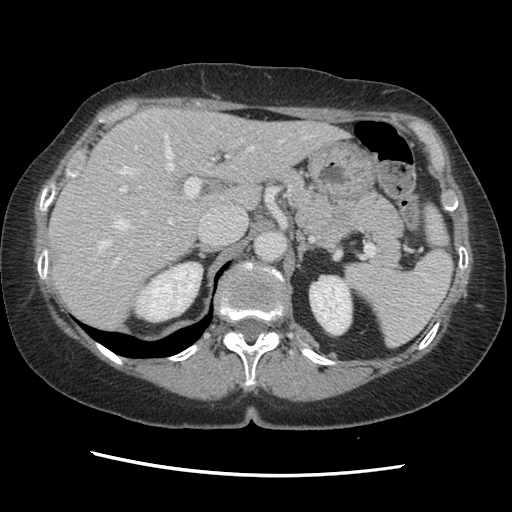
Contrast-enhanced abdominal CT, one axial slice. Slice 92 of 141 in the series (ordered by position). Soft-tissue window (W 400 / L 40 HU). 2.5 mm slice thickness. 512 × 512 image matrix. Female patient, age 61 years. Case-level facts recorded for this patient, not image findings: diagnosis: colorectal cancer liver metastases, imaged before liver resection; multiple liver metastases: no; largest metastasis: 2.4 cm; disease in both lobes: no.
Structures marked on this image (expert manual segmentation):
- hepatic veins: bounding box (x1, y1, x2, y2) in pixels: (94, 132, 312, 260)
- liver: (49, 109, 343, 332)
- planned liver remnant (the part of the liver to remain after resection): (49, 109, 343, 332)
- portal vein (with intrahepatic branches): (112, 146, 229, 267)